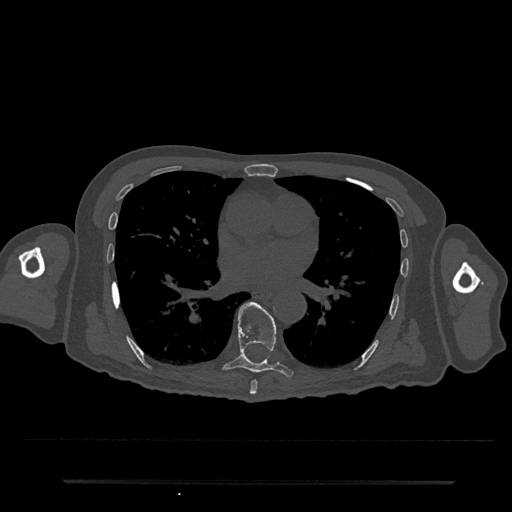
CT including the spine, one axial slice. Position 429 of 797 along the scan axis. Reconstruction kernel Br40s/3. 120 kVp. Bone window (W 1800 / L 400 HU). 0.5 mm slice thickness. 512 × 512 image matrix, field of view 427 × 427 mm. Male patient, age 74 years. From the clinical record (not read from this slice): primary cancer: prostate.
Outlined on this slice (semi-automatic segmentation, software-assisted and operator-edited):
- T7 vertebra: box from (x=250, y=380) to (x=258, y=395) px
- T8 vertebra: (x=222, y=302)–(x=293, y=379)